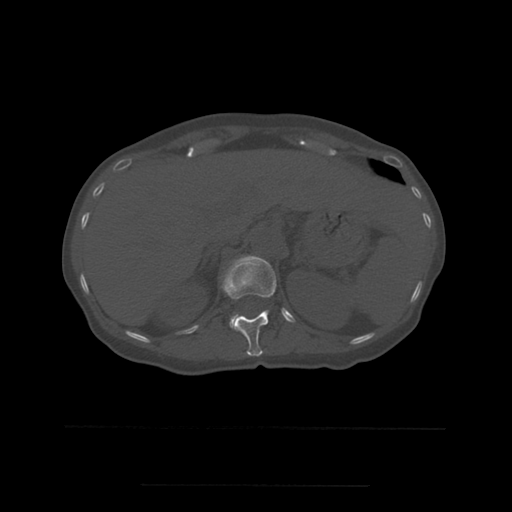
CT including the spine, one axial slice; position 253 of 544 along the scan axis; bone window (W 1800 / L 400 HU); 1.25 mm slice thickness; 512 × 512 image matrix. Patient age 58 years. Case-level facts recorded for this patient, not image findings: primary cancer: lung.
Annotated regions visible in this slice (semi-automatic segmentation, software-assisted and operator-edited):
- L1 vertebra: bounding box <230,316,237,329> (left, top, right, bottom; pixels)
- T12 vertebra: <222,256,277,357>